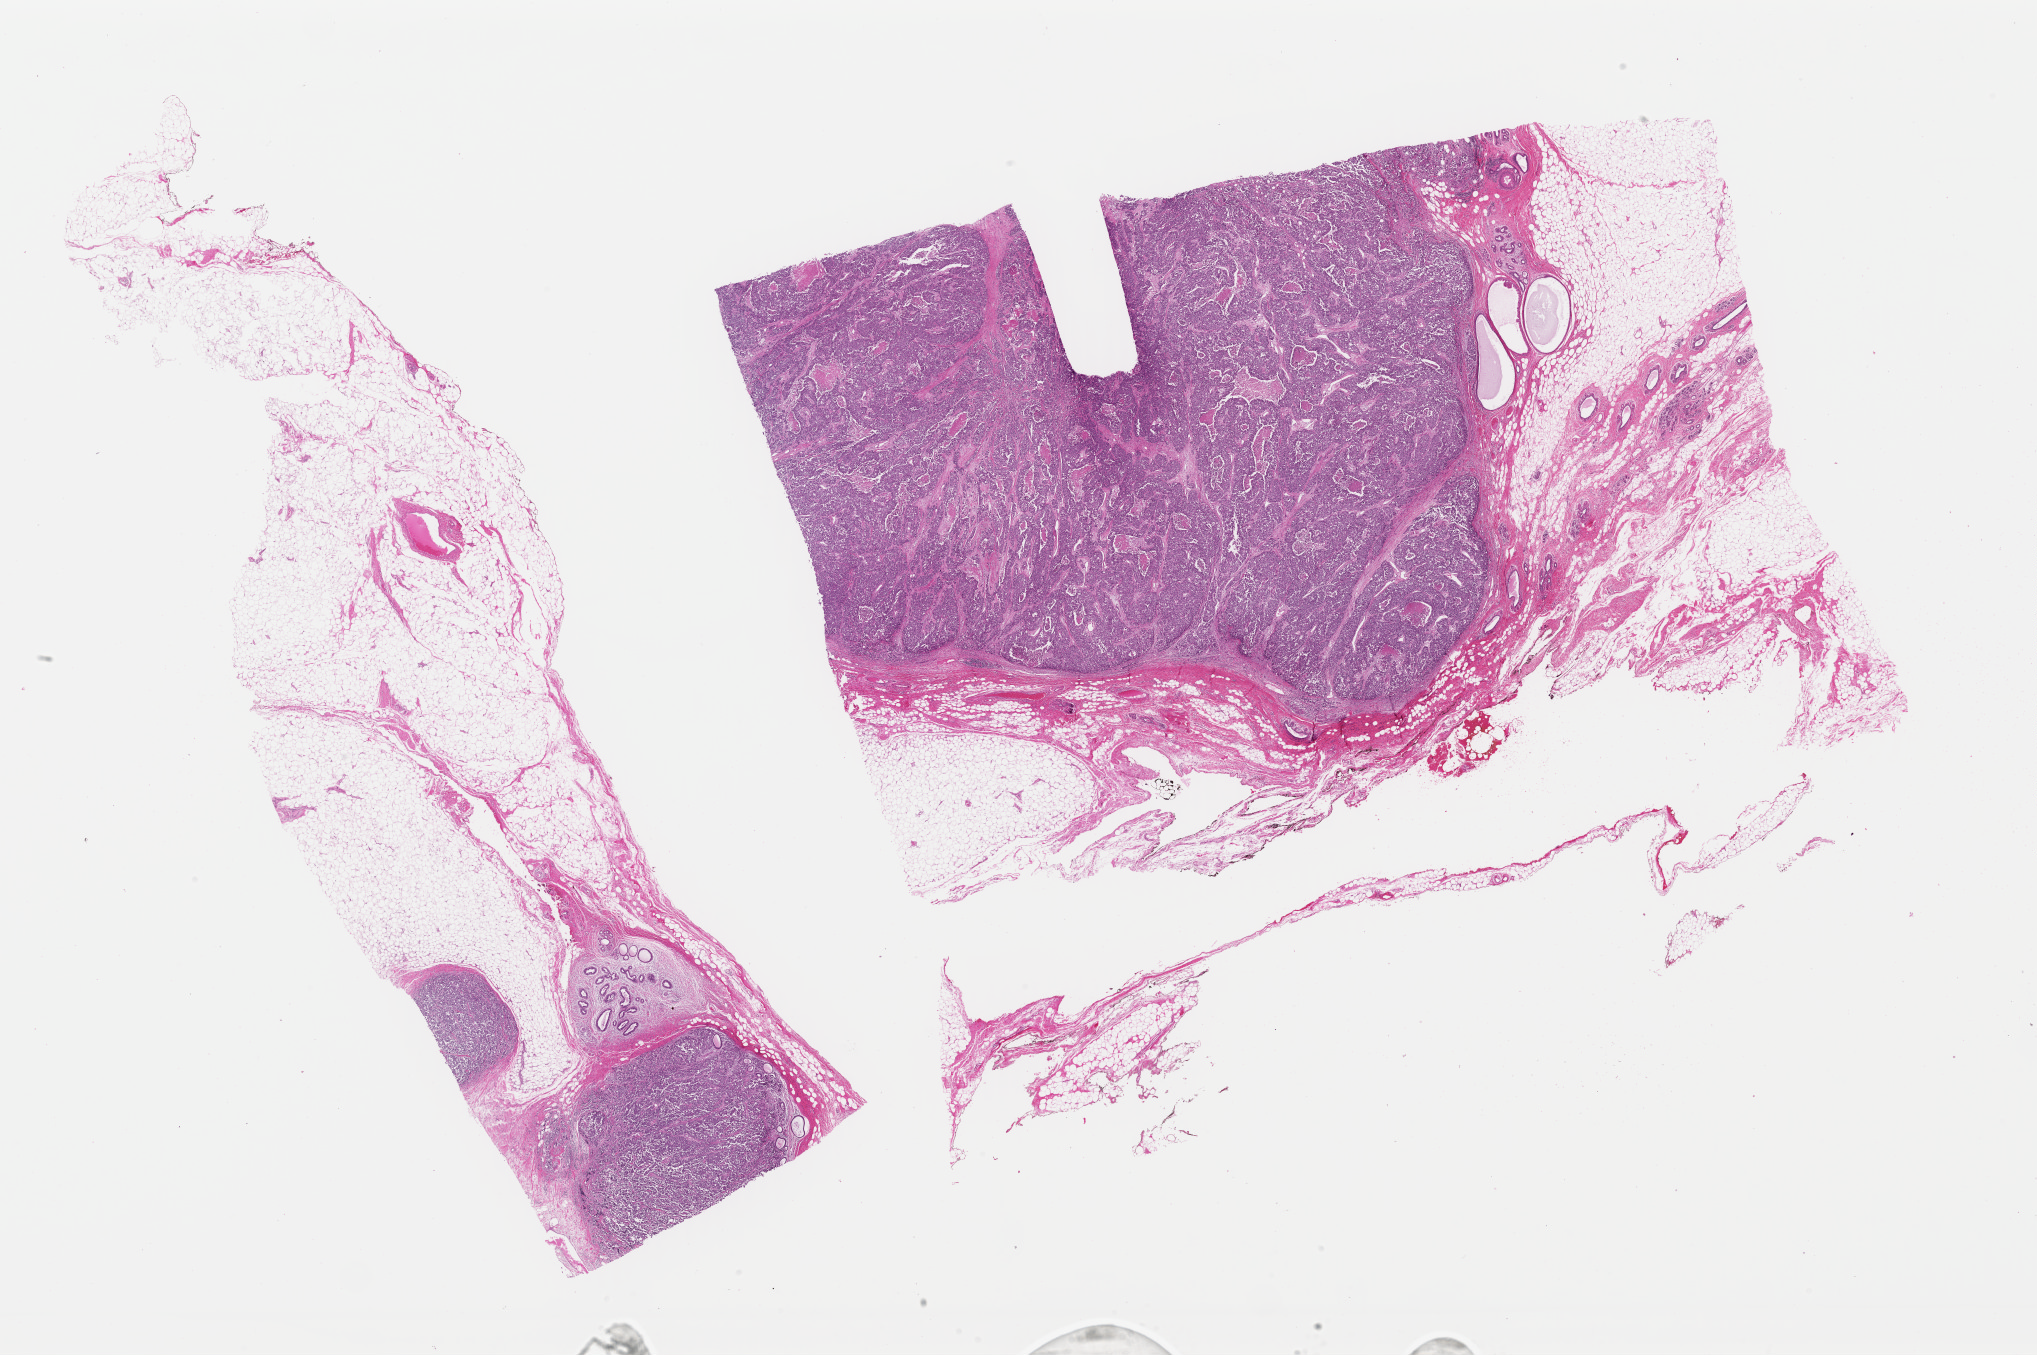
Hematoxylin and eosin (H&E) stained whole-slide image — whole scanned area (about 32.1 x 21.4 mm) shown as a low-resolution overview, formalin-fixed paraffin-embedded (FFPE) diagnostic section, sample: primary tumour, breast. Female patient; age at initial diagnosis 47 years.
• TNM: T2 N0 (i+) M0
• AJCC pathologic stage: IIA (6th edition)
• lymph nodes positive (case pathology): 0 of 3 examined
• histologic diagnosis: Infiltrating duct carcinoma, NOS